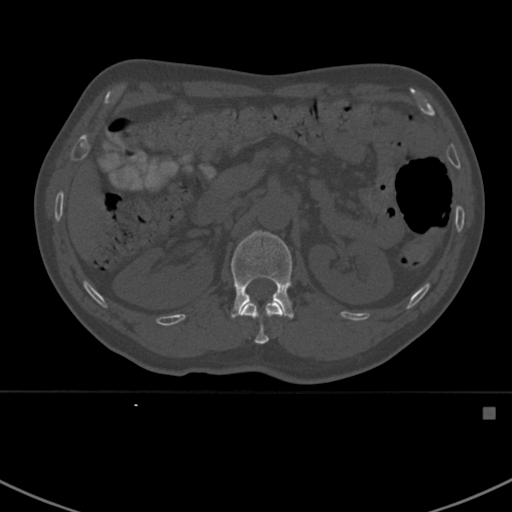
CT including the spine, one axial slice. Position 316 of 412 along the scan axis. 120 kVp. Bone window (W 1800 / L 400 HU). 1.5 mm slice thickness. 512 × 512 image matrix, field of view 358 × 358 mm. Patient: male, 59 years. From the clinical record (not read from this slice): primary cancer: prostate.
Outlined on this slice (semi-automatically segmented with operator editing):
- L1 vertebra: box from (x=230, y=231) to (x=315, y=318) px
- T12 vertebra: (x=242, y=303)–(x=282, y=344)